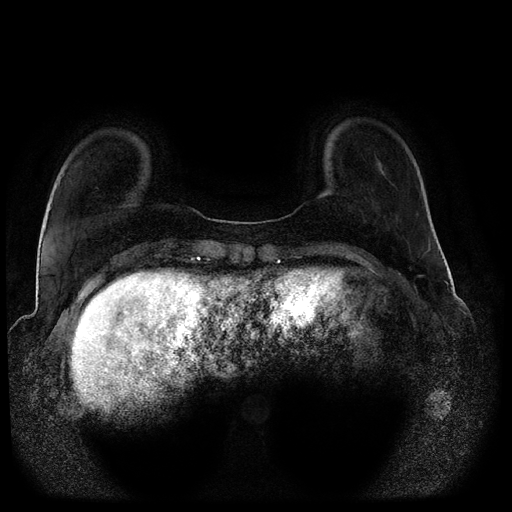
Breast MRI (dynamic contrast-enhanced, multi-phase), one axial slice. Position 25 of 116 along the scan axis. Dynamic contrast-enhanced series, time point 2 of 5 at this slice position (early post-contrast). 1.5 T. TE 2.6 ms, TR 5.3 ms. 512 × 512 image matrix. Patient: female, 44 years.
Structures marked on this image (semi-automatically segmented with operator editing):
- breast lesion (labelled benign in the annotation): bounding box (x1, y1, x2, y2) in pixels: (378, 163, 385, 175)